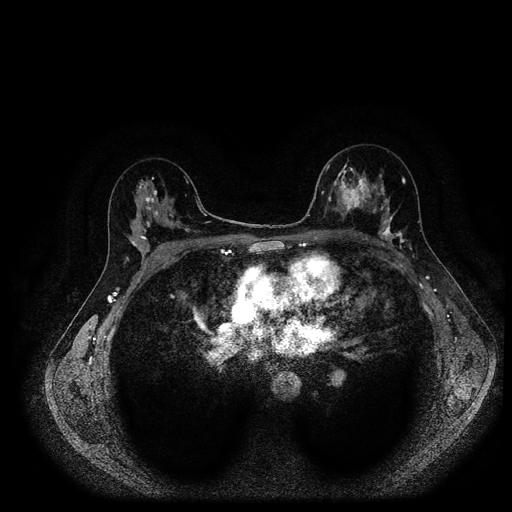
Breast MRI (dynamic contrast-enhanced, multi-phase), one axial slice. Position 60 of 116 along the scan axis. Dynamic contrast-enhanced series, time point 2 of 5 at this slice position (early post-contrast). 1.5 T. TE 2.7 ms, TR 5.4 ms. 512 × 512 image matrix. Patient: female, 40 years.
Annotated regions visible in this slice (semi-automatically segmented with operator editing):
- breast lesion (labelled 'tumour' in the annotation; benign lesions carry a separate 'benign' label): bounding box <334,167,371,215> (left, top, right, bottom; pixels)